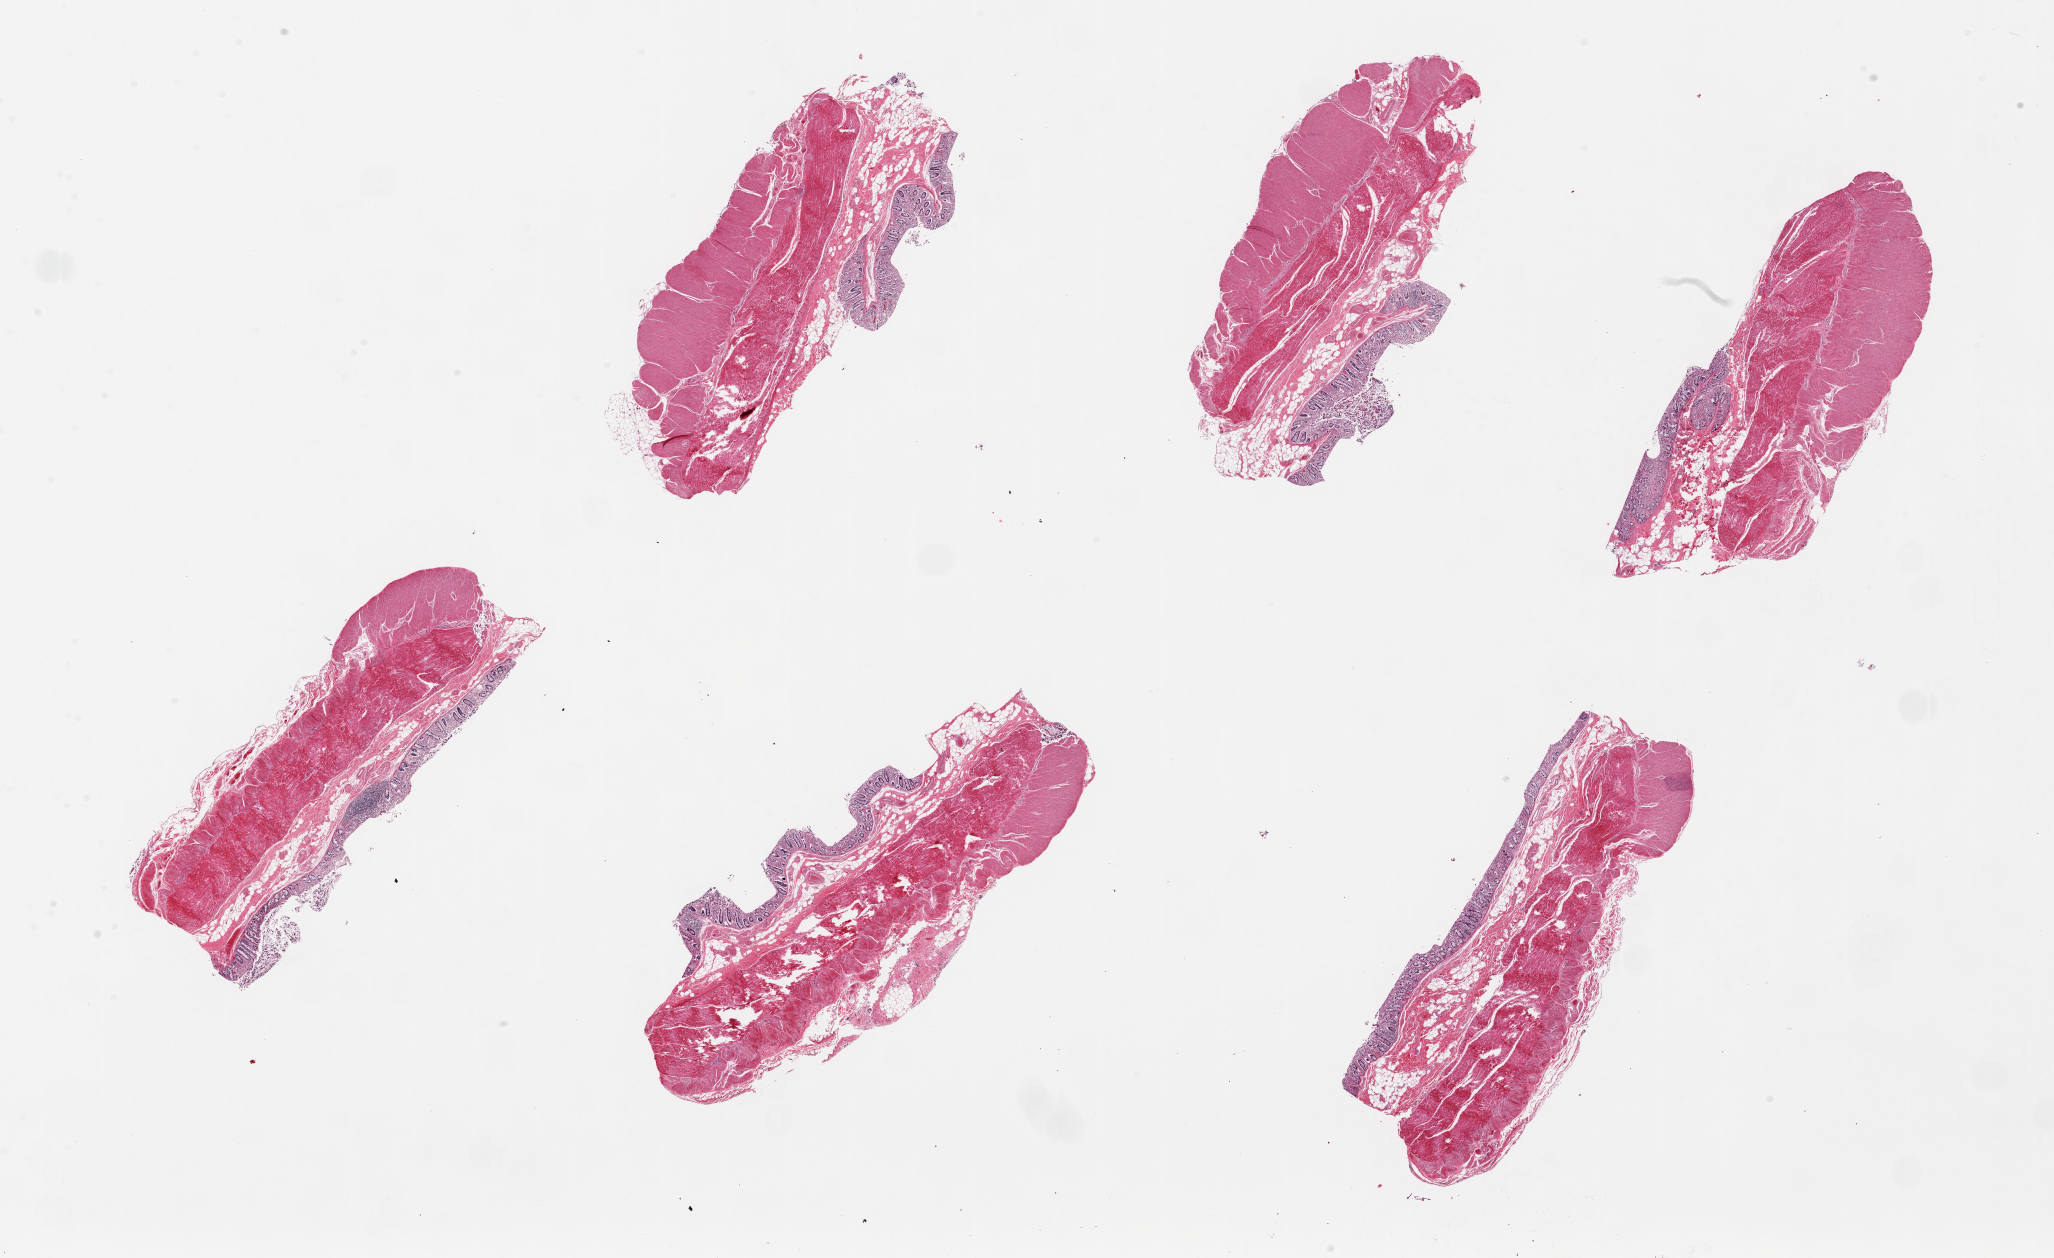
Digitized H&E-stained section, whole scanned area (about 32.5 x 19.9 mm) shown as a low-resolution overview, PAXgene-fixed paraffin-embedded (PFPE) section, sampled site (target tissue): transverse colon, donor tissue sample. Male donor.
Reviewer comment on this tissue sample: 6 pieces; up to 9x4mm; Mucosa in one aliquot, ~10% thickness but badly autolyzed.